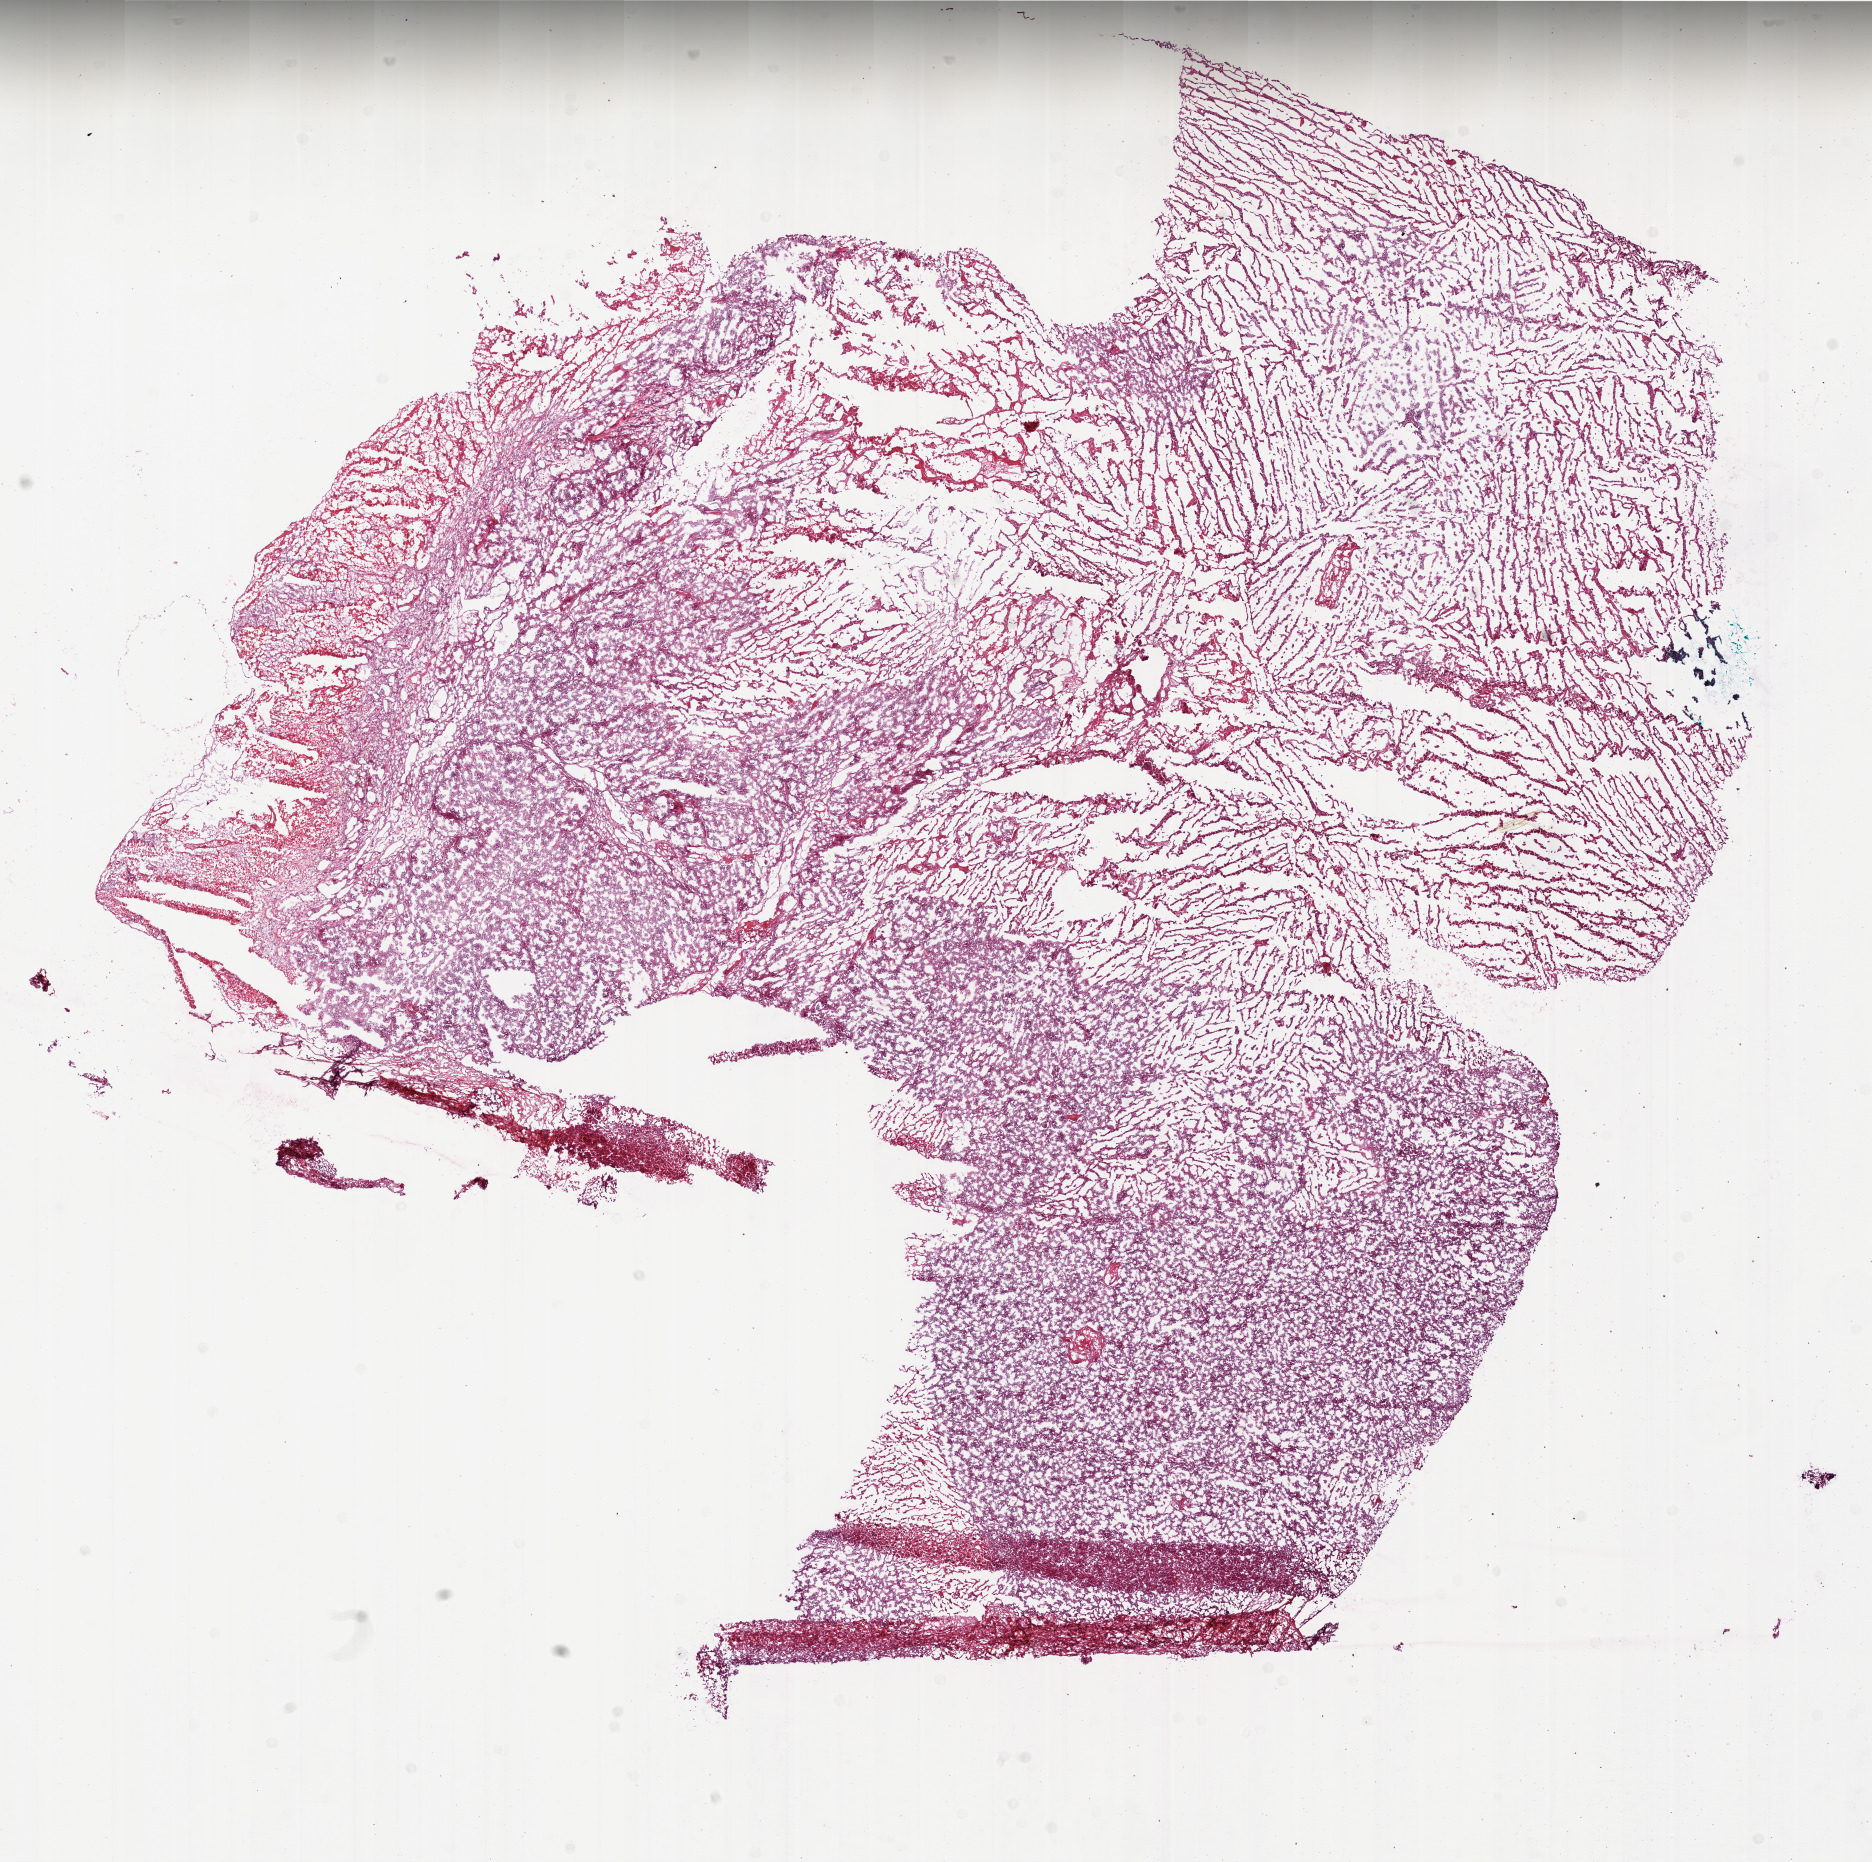
Hematoxylin and eosin (H&E) stained whole-slide image, shown as a low-resolution overview of the whole scanned area (about 15.0 x 14.9 mm, slide scanned at 20x). Frozen section from the bottom of the tissue portion. Sample: primary tumour, brain. Male, age 40 years at initial diagnosis. Pathologist review of this section (percent, as recorded): tumour cells 60%, tumour nuclei 100%, normal cells 0%, stromal cells 0%, necrosis 40%. Inflammatory infiltration, as recorded: lymphocyte infiltration 0%.
Histologic diagnosis: Glioblastoma.